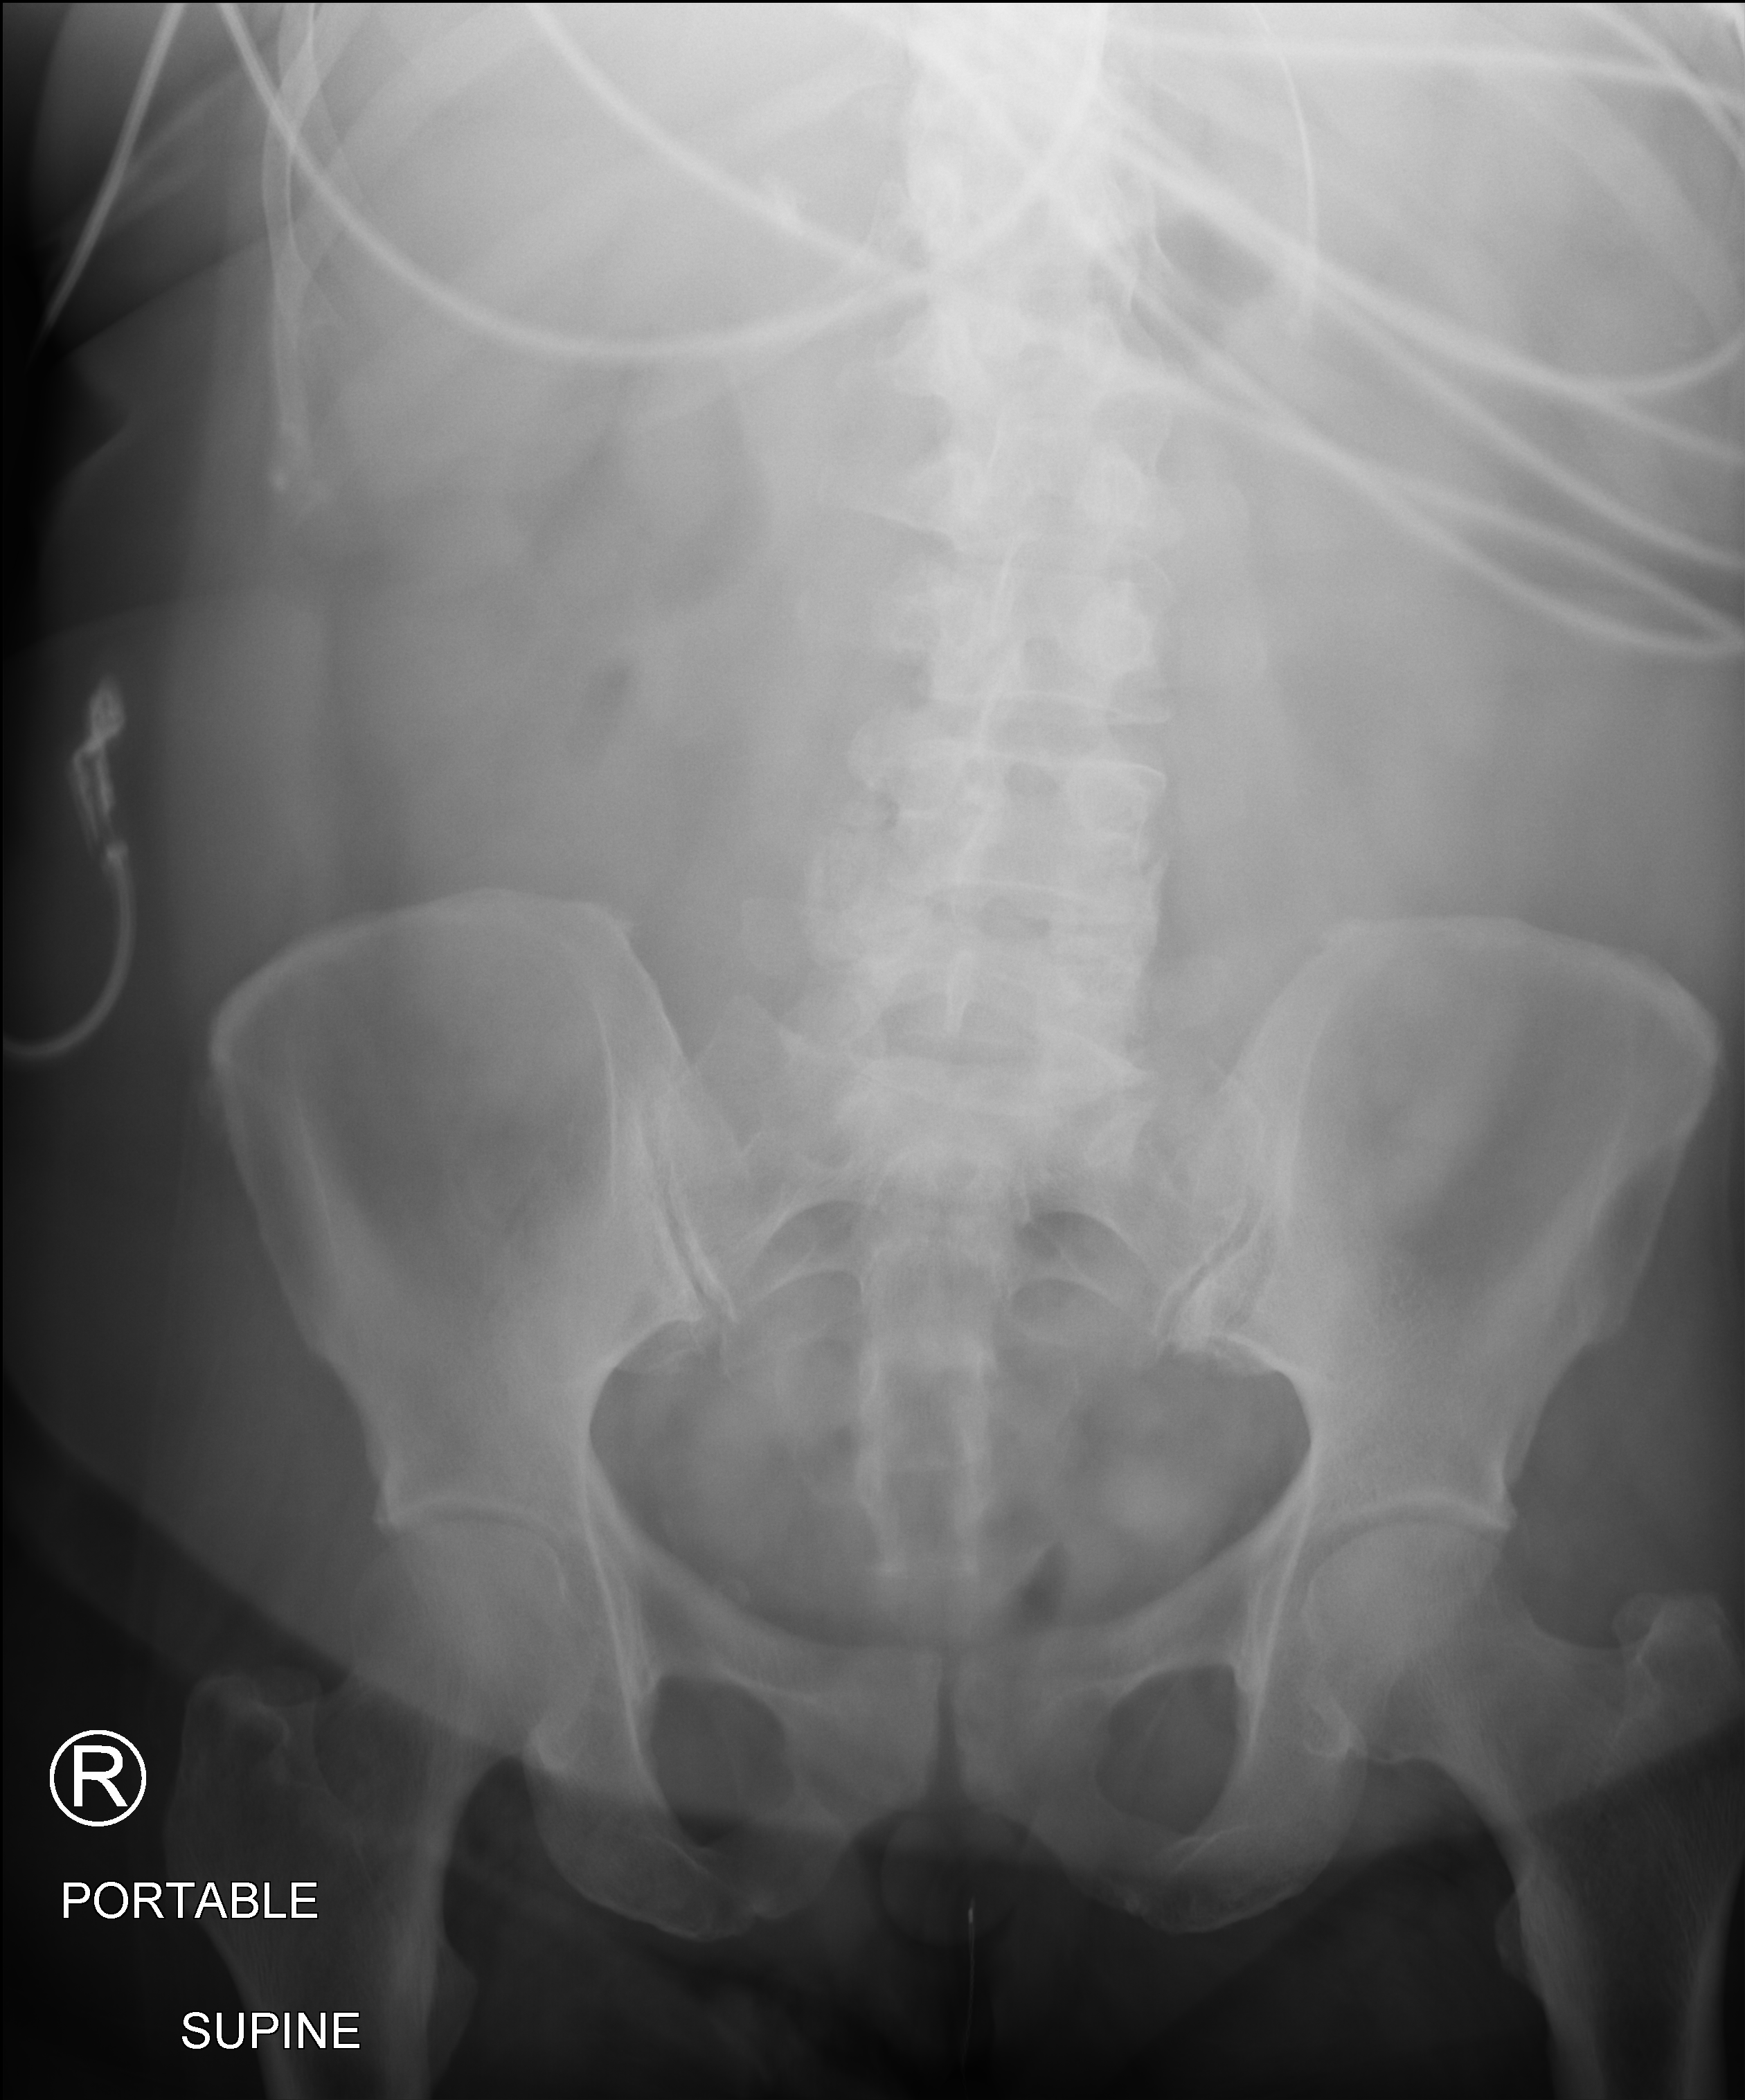
Abdomen X-ray (portable), anteroposterior (AP) projection. Female patient hospitalised with COVID-19, age 60–74 years.
Admission-level facts for this patient (not findings on this image; timing relative to this image not recorded):
- other chronic lung disease (admission record): yes